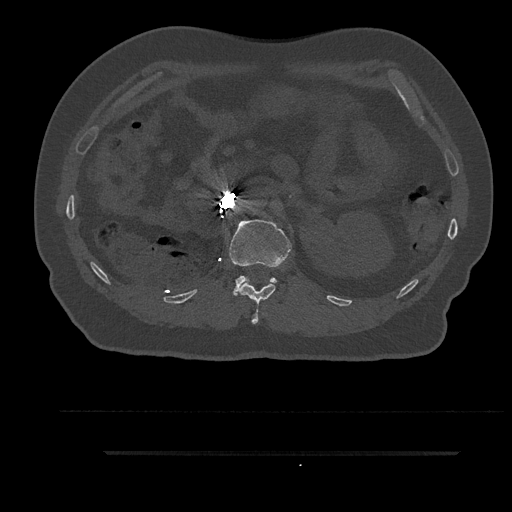
CT including the spine, one axial slice. Position 204 of 797 along the scan axis. Reconstruction kernel Br40s/3. 120 kVp. Bone window (W 1800 / L 400 HU). 512 × 512 image matrix. Male patient, age 63 years. From the clinical record (not read from this slice): primary cancer: renal; vertebrae with lytic lesions (as recorded): T8.
Outlined on this slice (semi-automatically segmented with operator editing):
- L1 vertebra: bounding box <229,219,292,295> (left, top, right, bottom; pixels)
- T12 vertebra: <239,281,276,325>